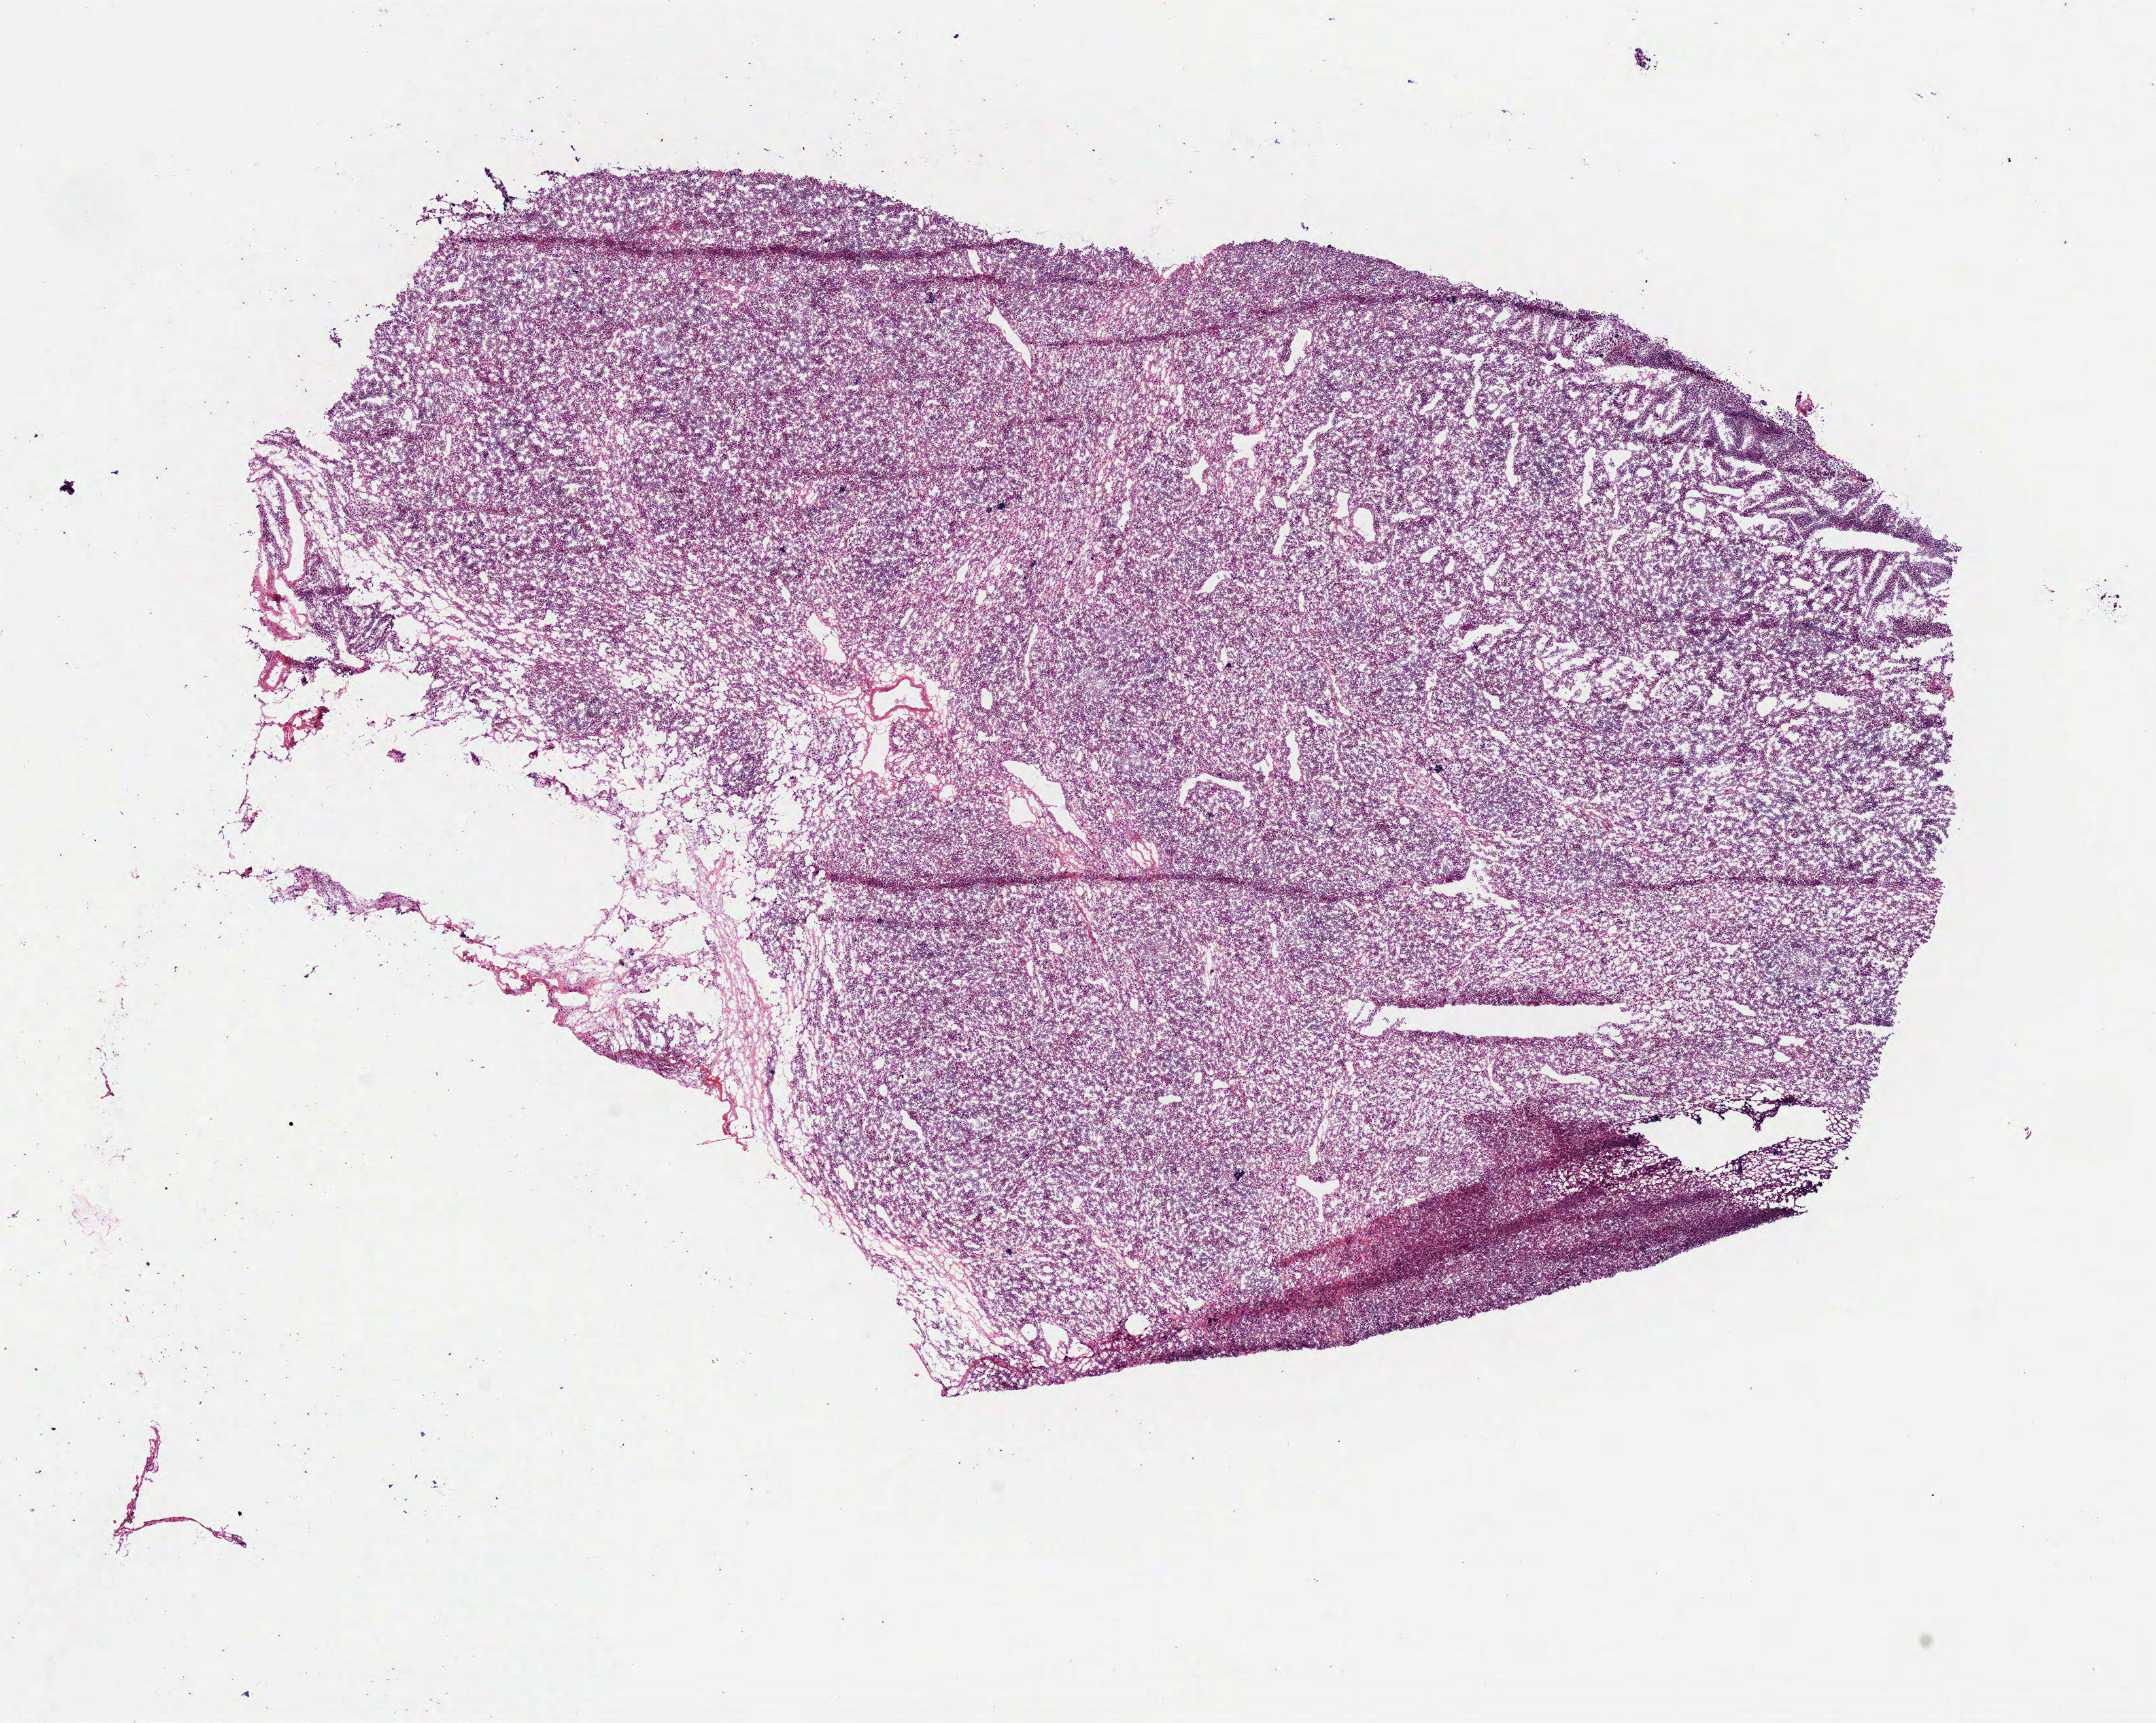
Digitized Hematoxylin and eosin (H&E) stained tissue section (whole slide), shown as a low-resolution overview of the whole scanned area (about 13.3 x 10.6 mm, slide scanned at 40x). Frozen section. Primary tumour sample from the stomach. Male patient; age at initial diagnosis 59 years. Histologic grade: G3 (poorly differentiated). Slide review estimates, as recorded: tumour cells 100%, tumour nuclei 85%, normal cells 0%, stromal cells 0%, necrosis 0%. Infiltration values recorded for this section: lymphocyte infiltration 10%, monocyte infiltration 0%, neutrophil infiltration 0%.
Diagnosis: Carcinoma, diffuse type (cardia, NOS). Lymph nodes positive (case pathology): 21 of 24 examined.